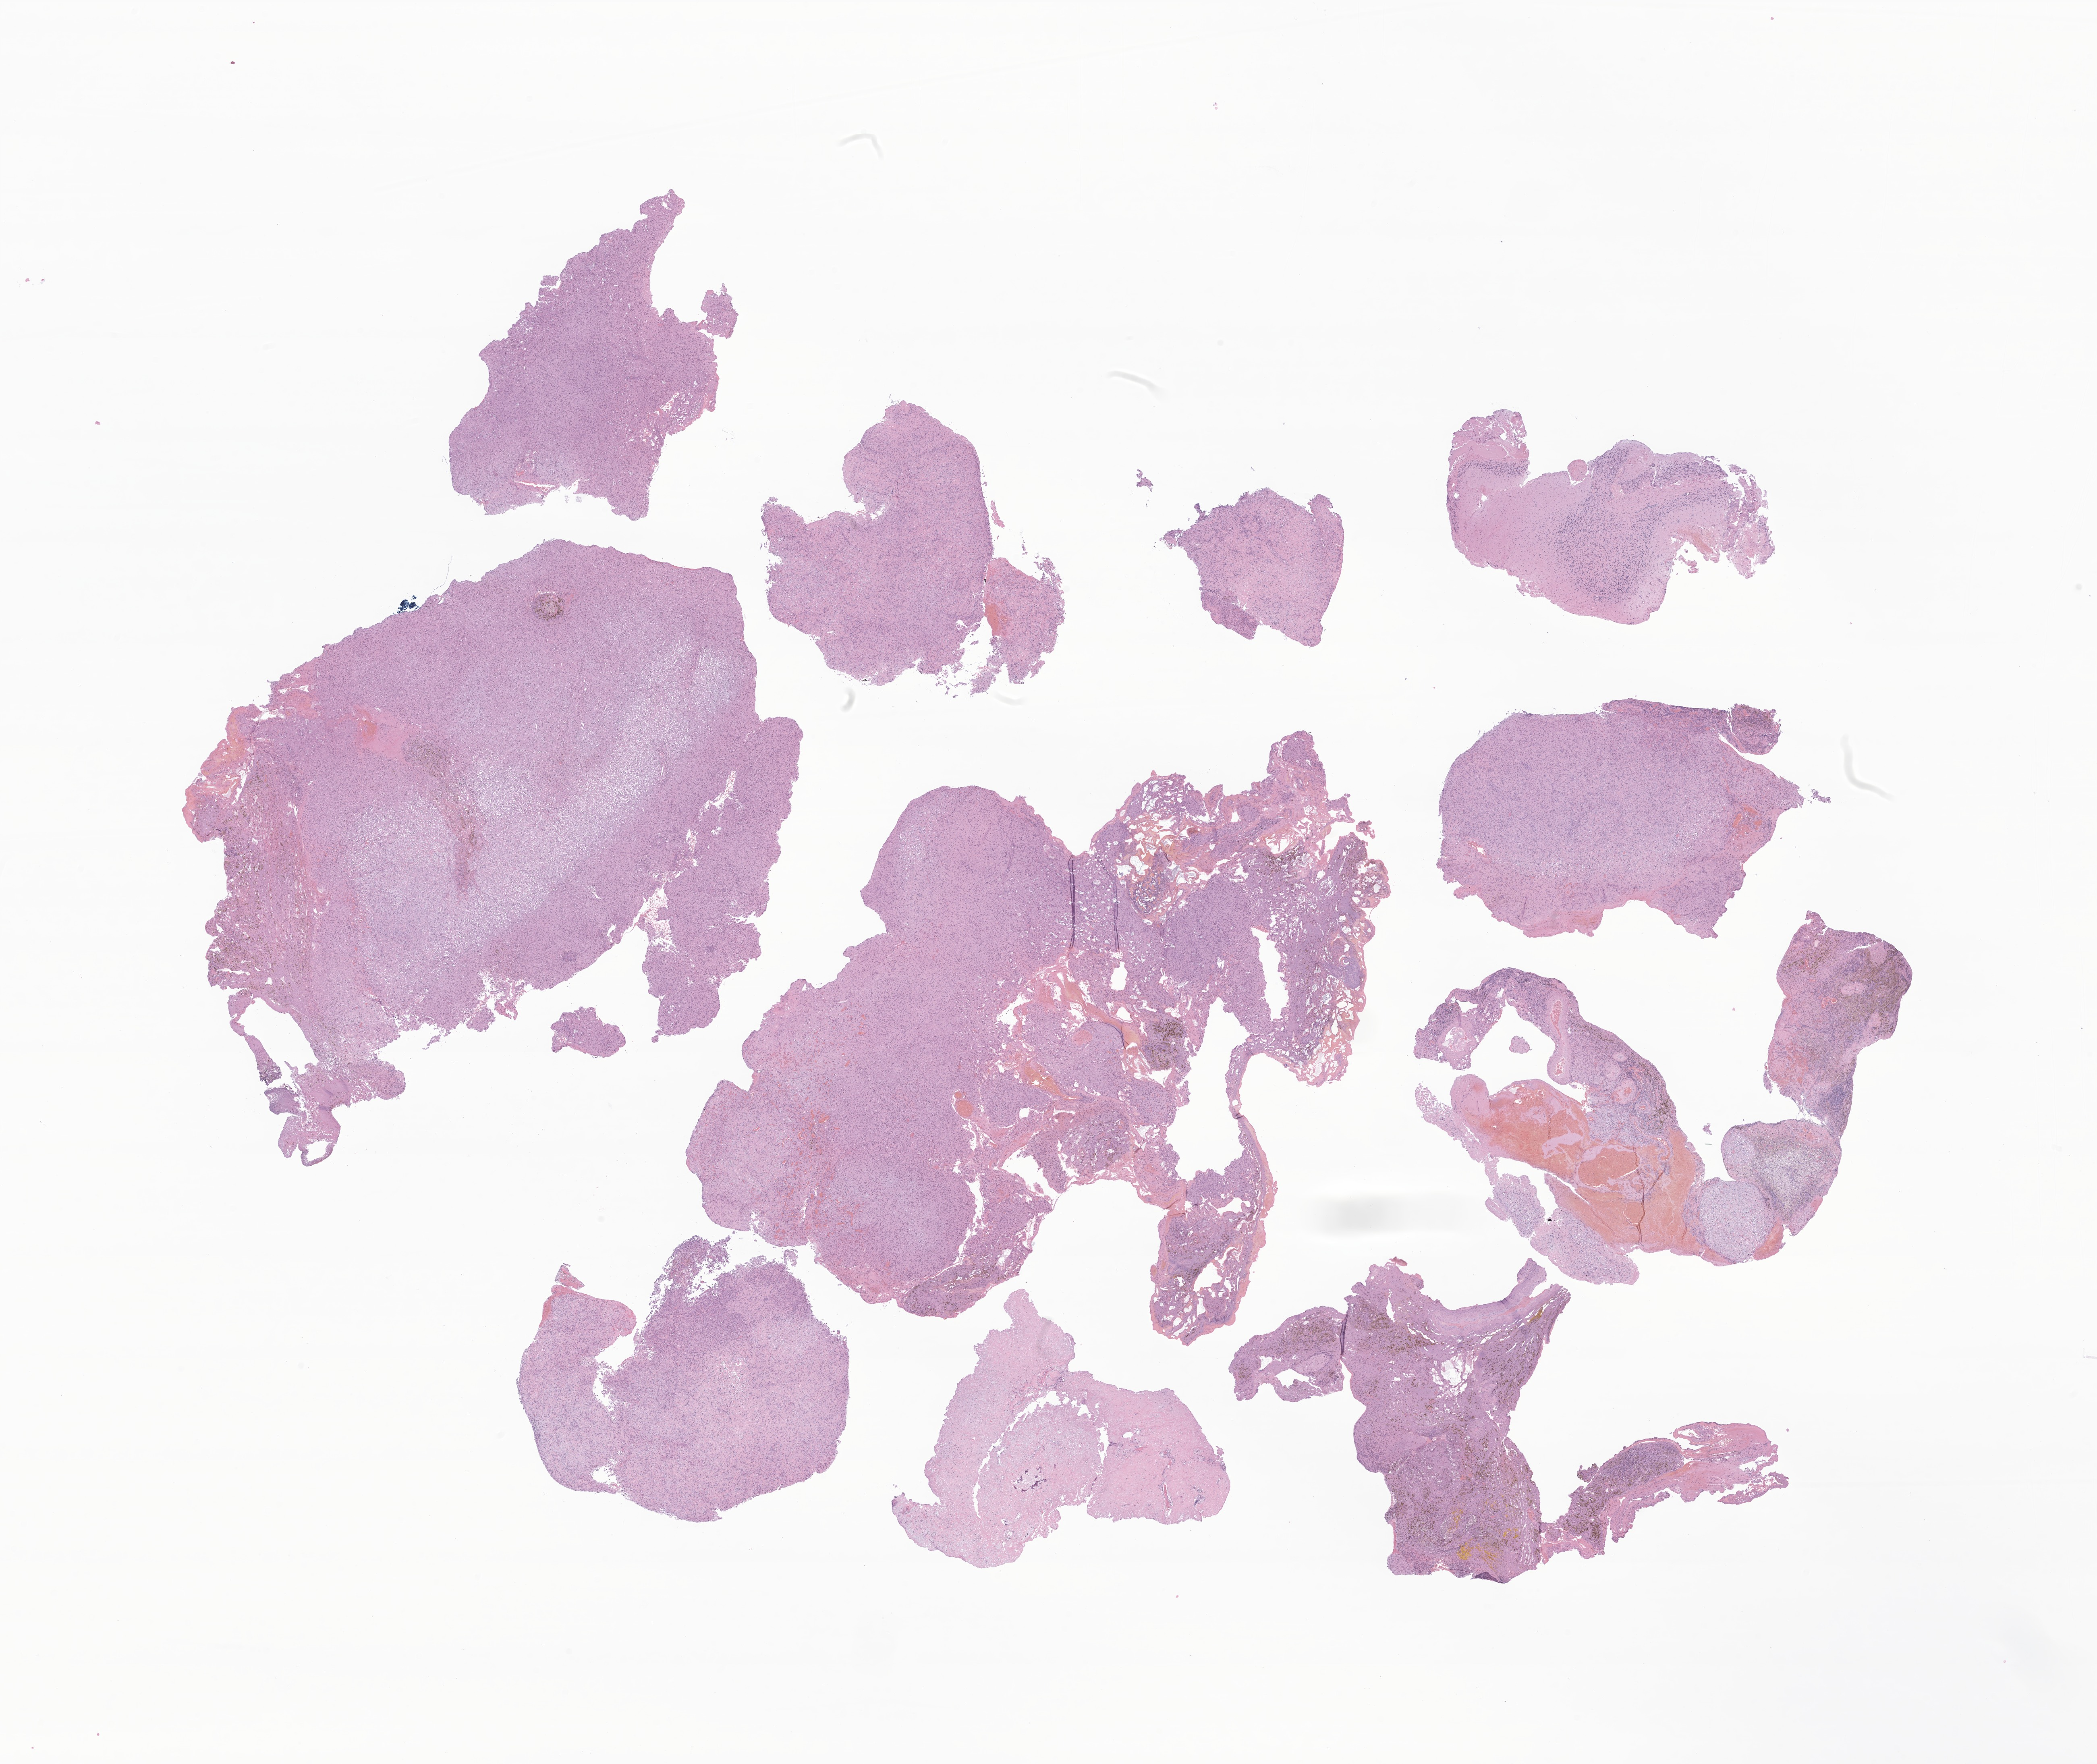
Whole-slide image, H&E stain of tumor tissue from the brain, shown as a low-resolution overview of the whole scanned area (about 21.9 x 18.5 mm). FFPE section. Patient male; age 218 months (18 years 2 months).
Diagnosis (ICD-O-3 morphology term): Sarcoma, NOS.